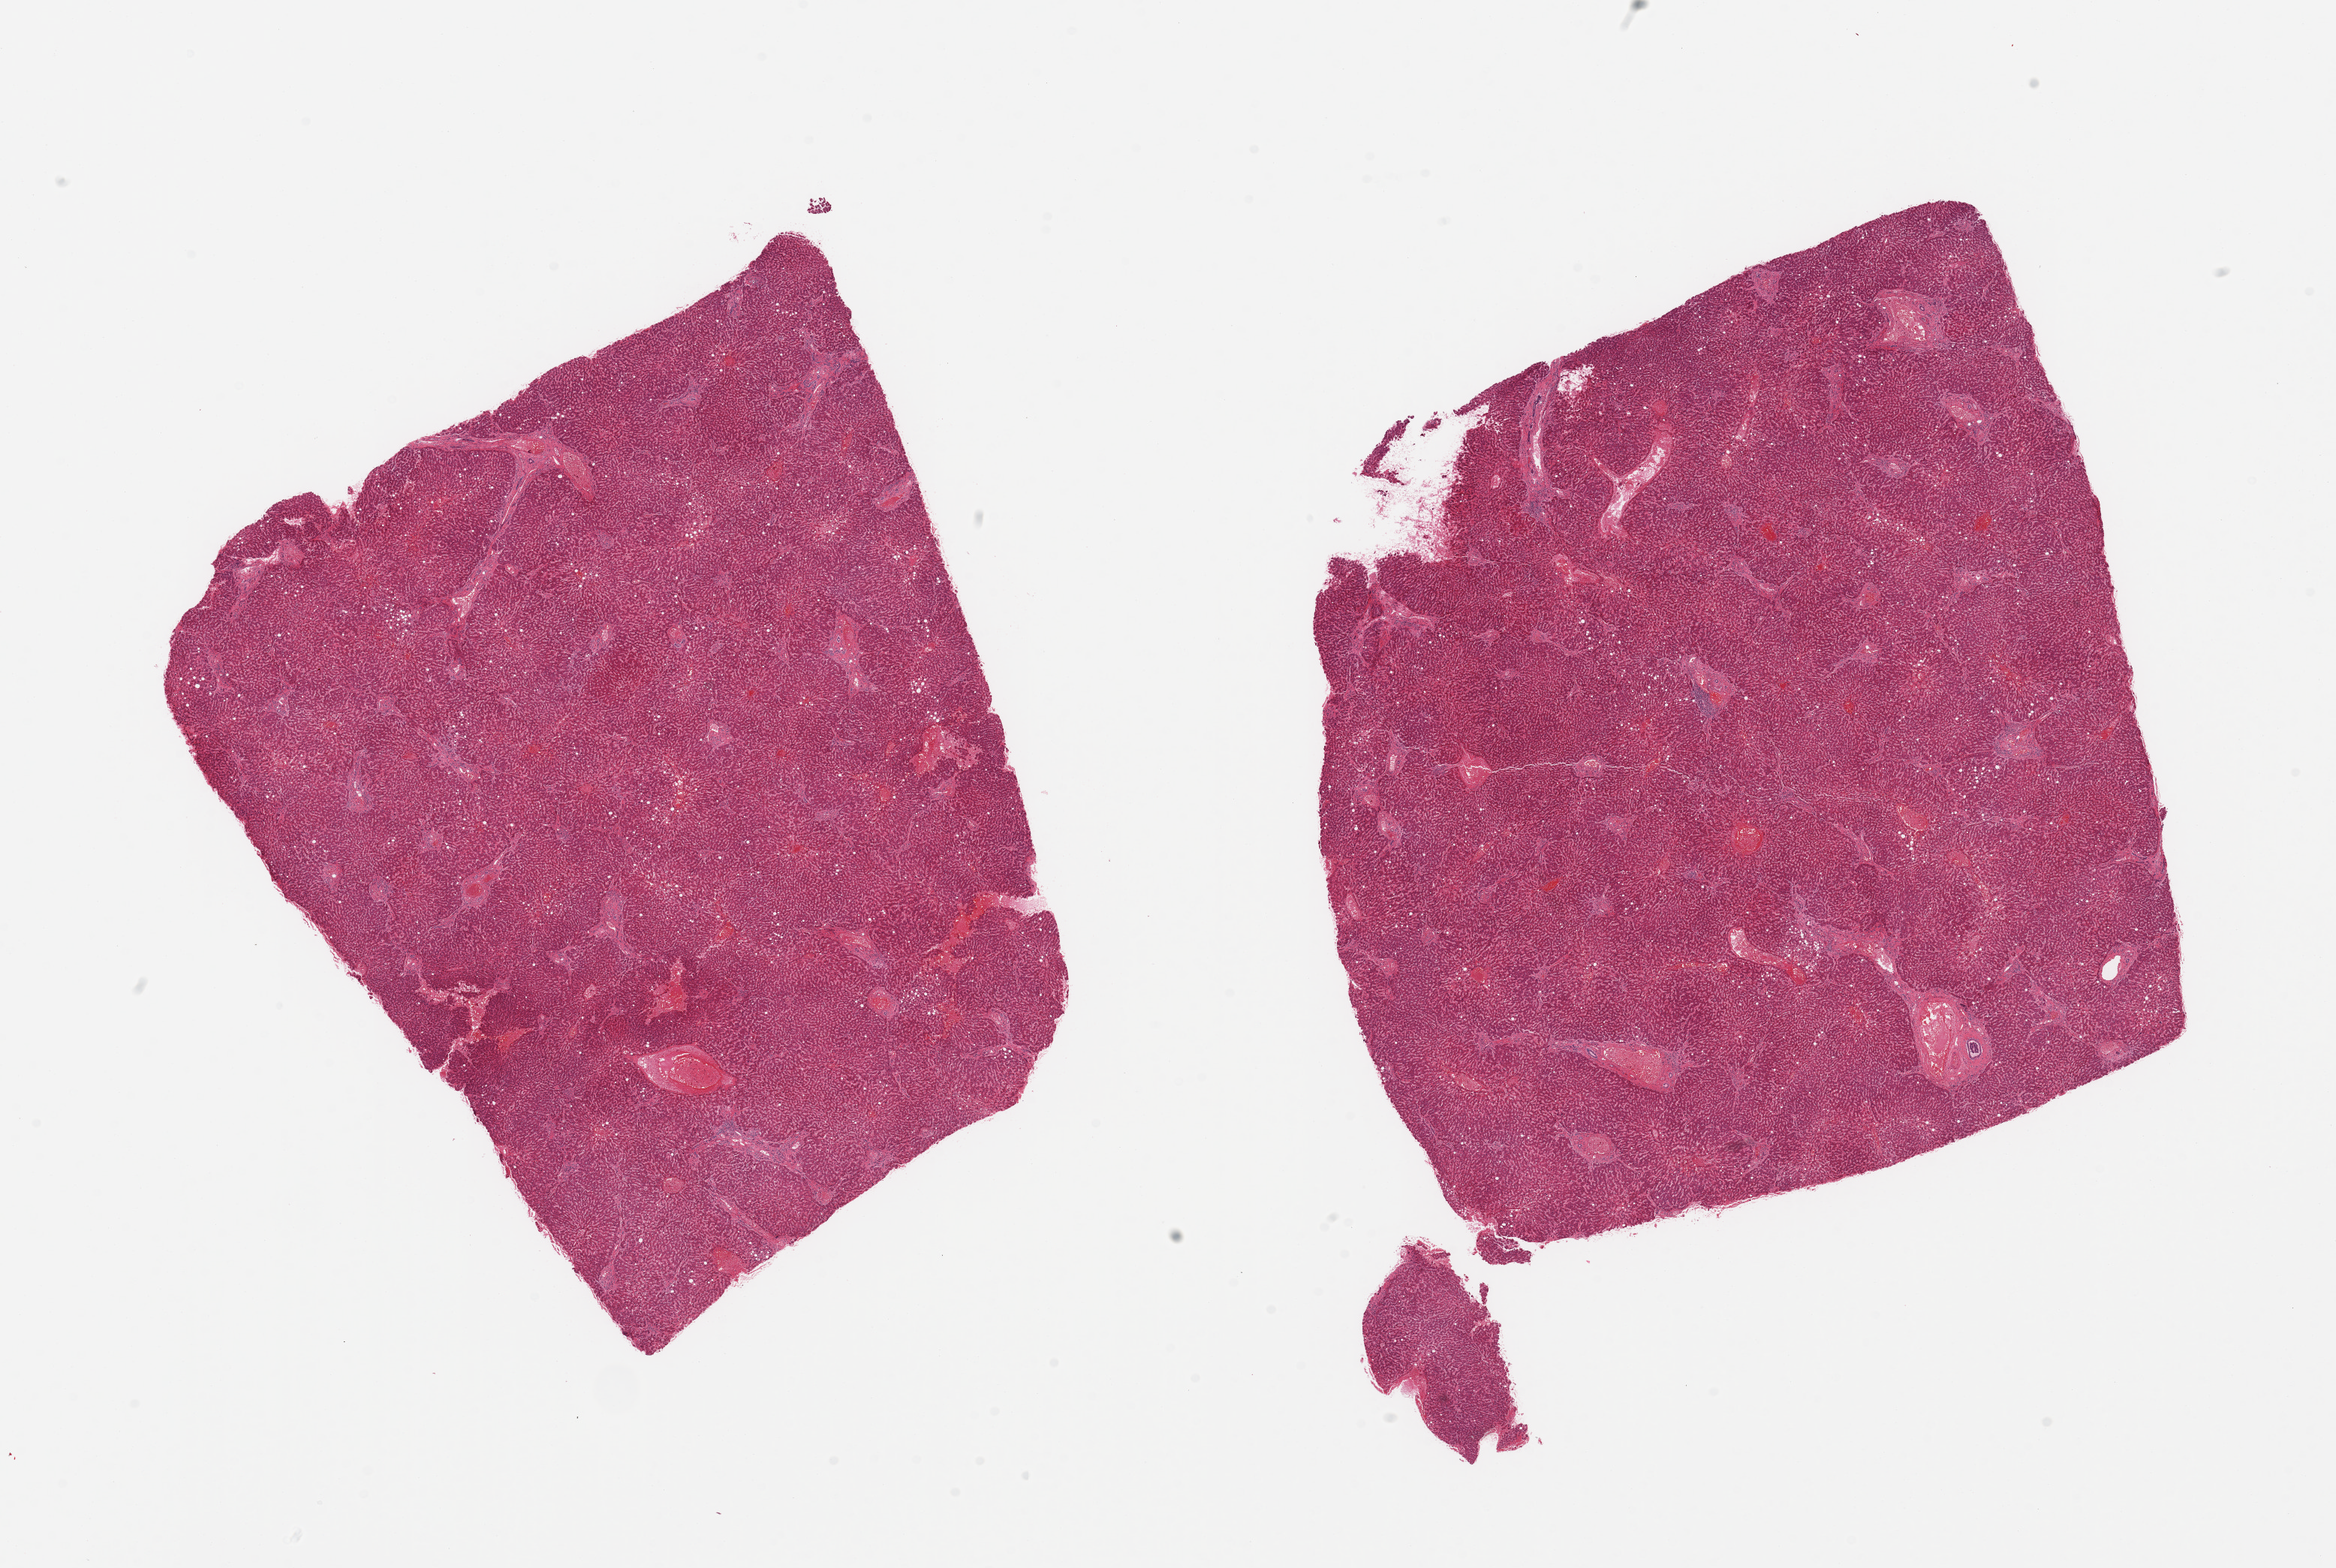
Hematoxylin and eosin (H&E) whole-slide image, low-resolution overview of the scanned area, about 24.6 x 16.5 mm; PAXgene-fixed paraffin-embedded (PFPE) section; target tissue: liver; donor tissue sample. Donor: male.
- reviewer comment on this tissue sample: 2 pieces; minimal central congestion; 10% macrovesicular steatosis